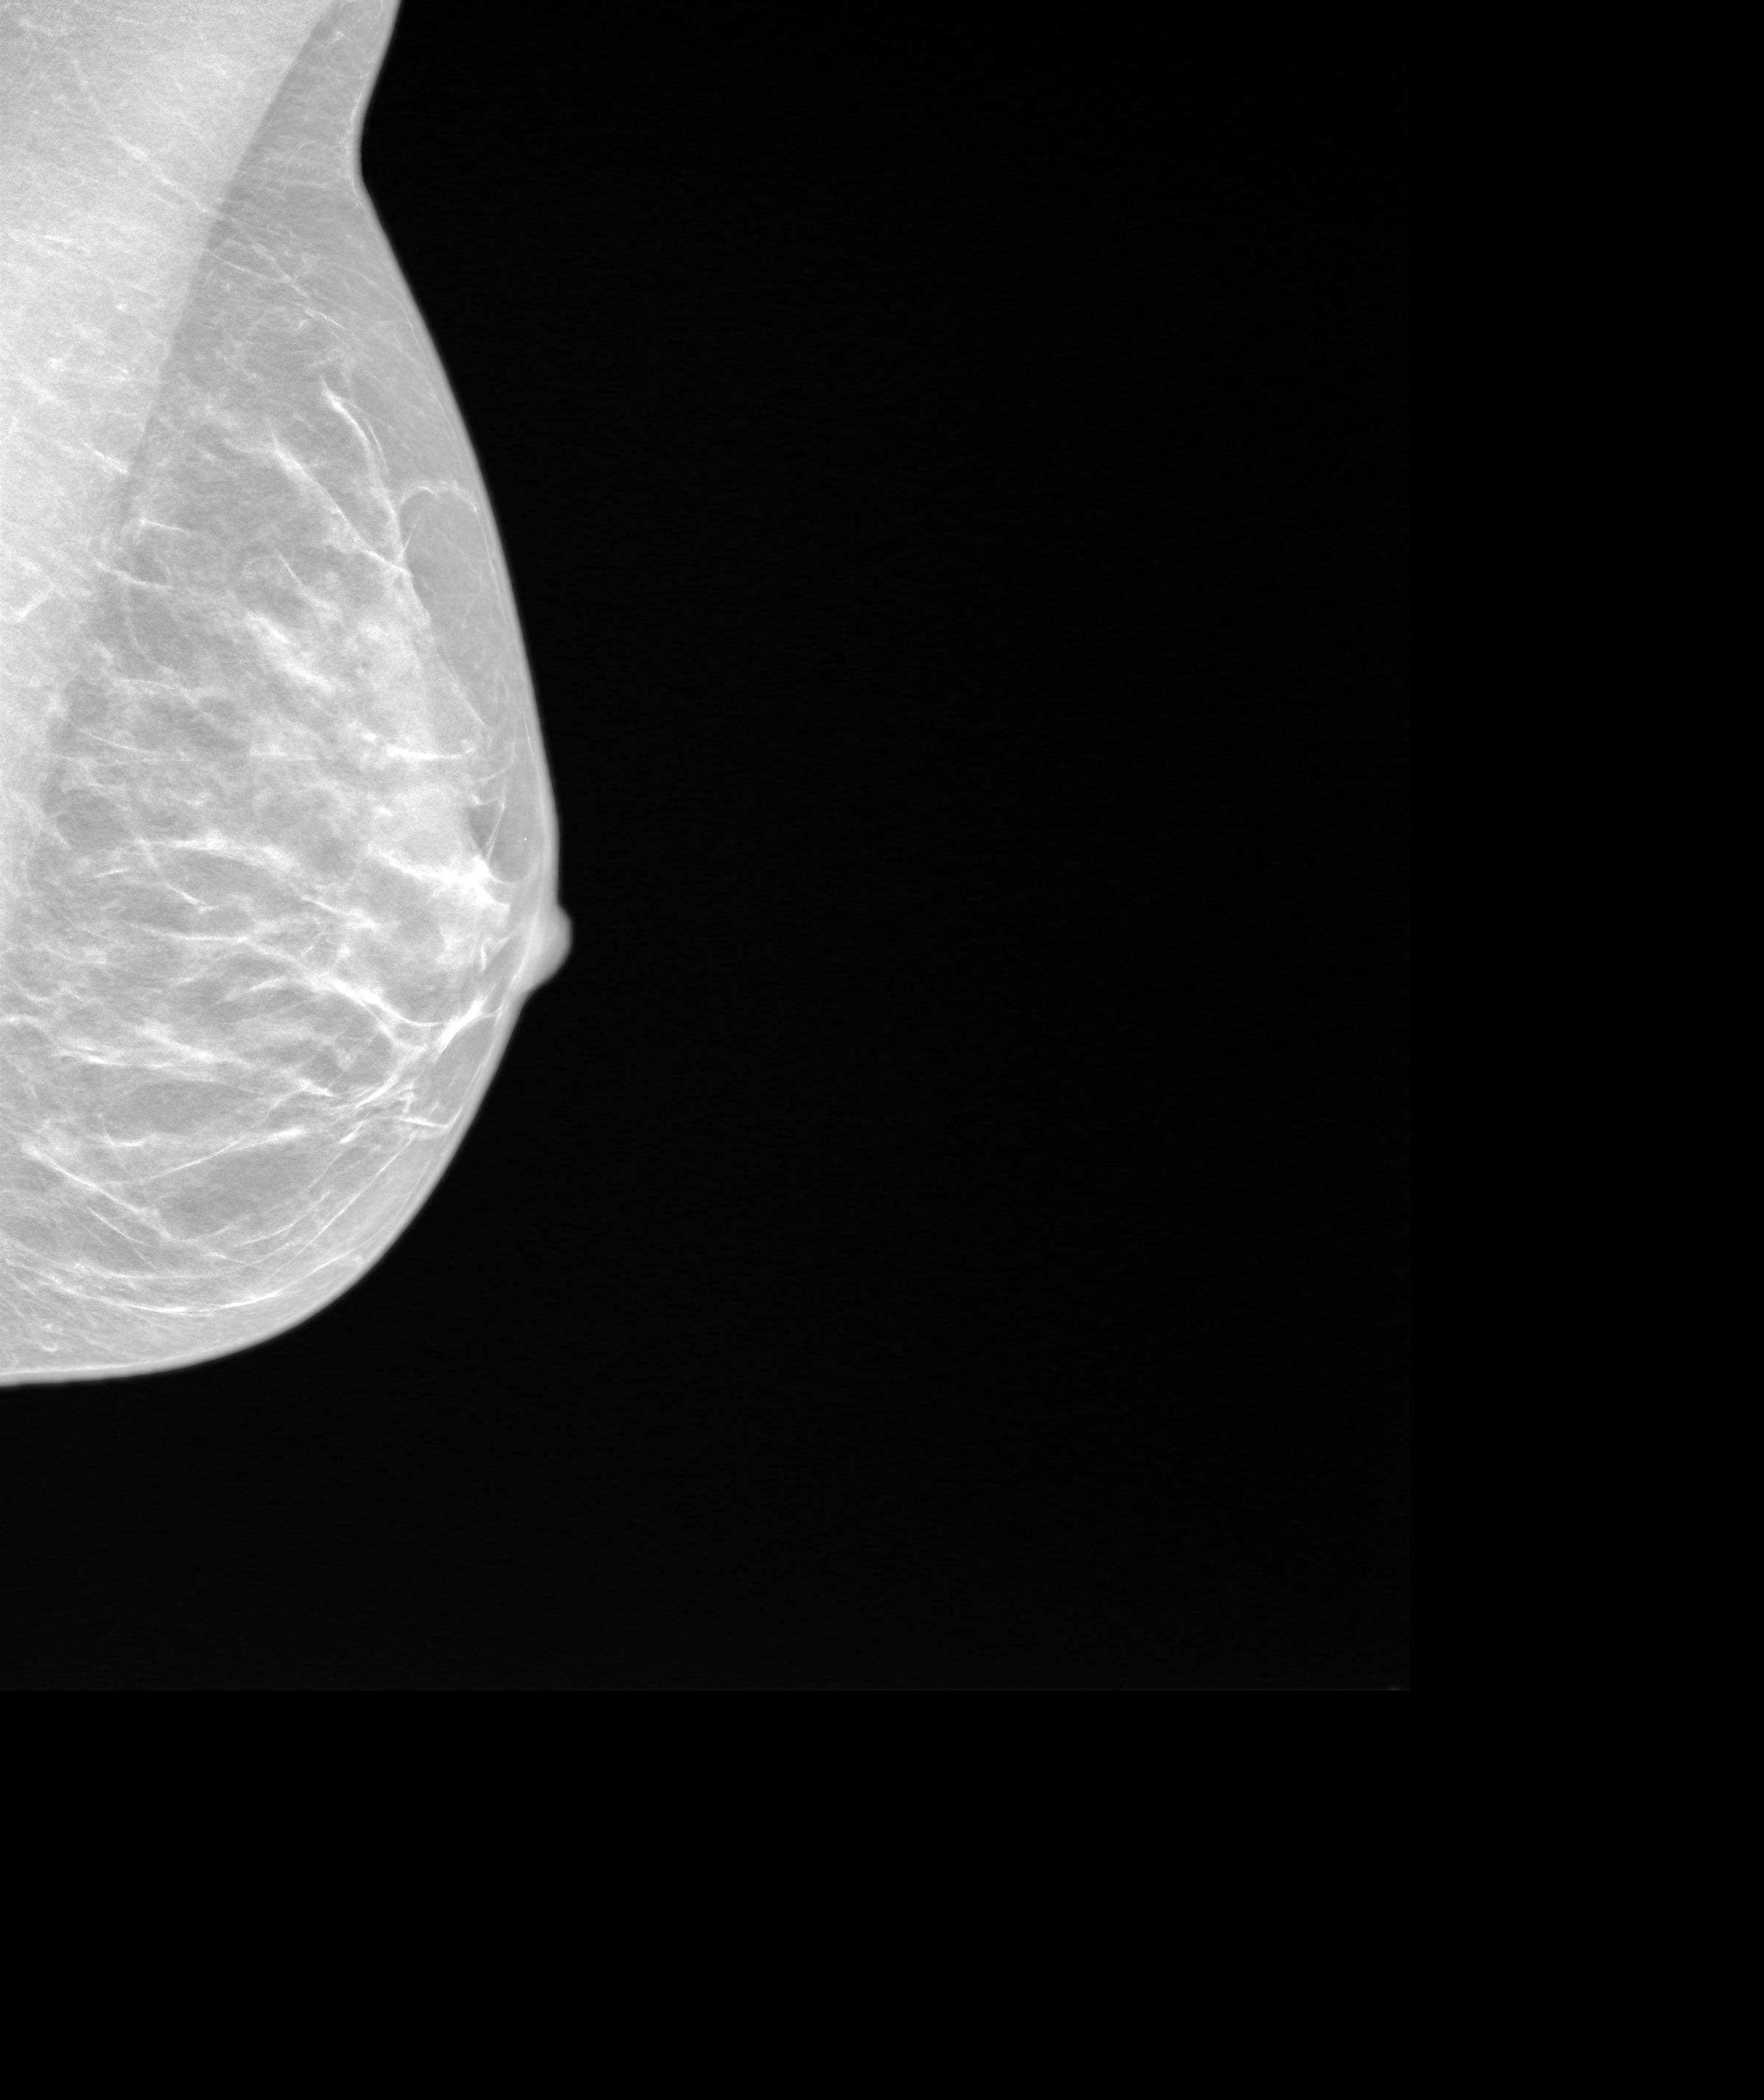
Screening examination, system: SenoIris_1SP2(440). Female patient, age 66 years.
Image type: synthesized 2-D view from tomosynthesis. Breast: left. Projection: mediolateral oblique (MLO) view.